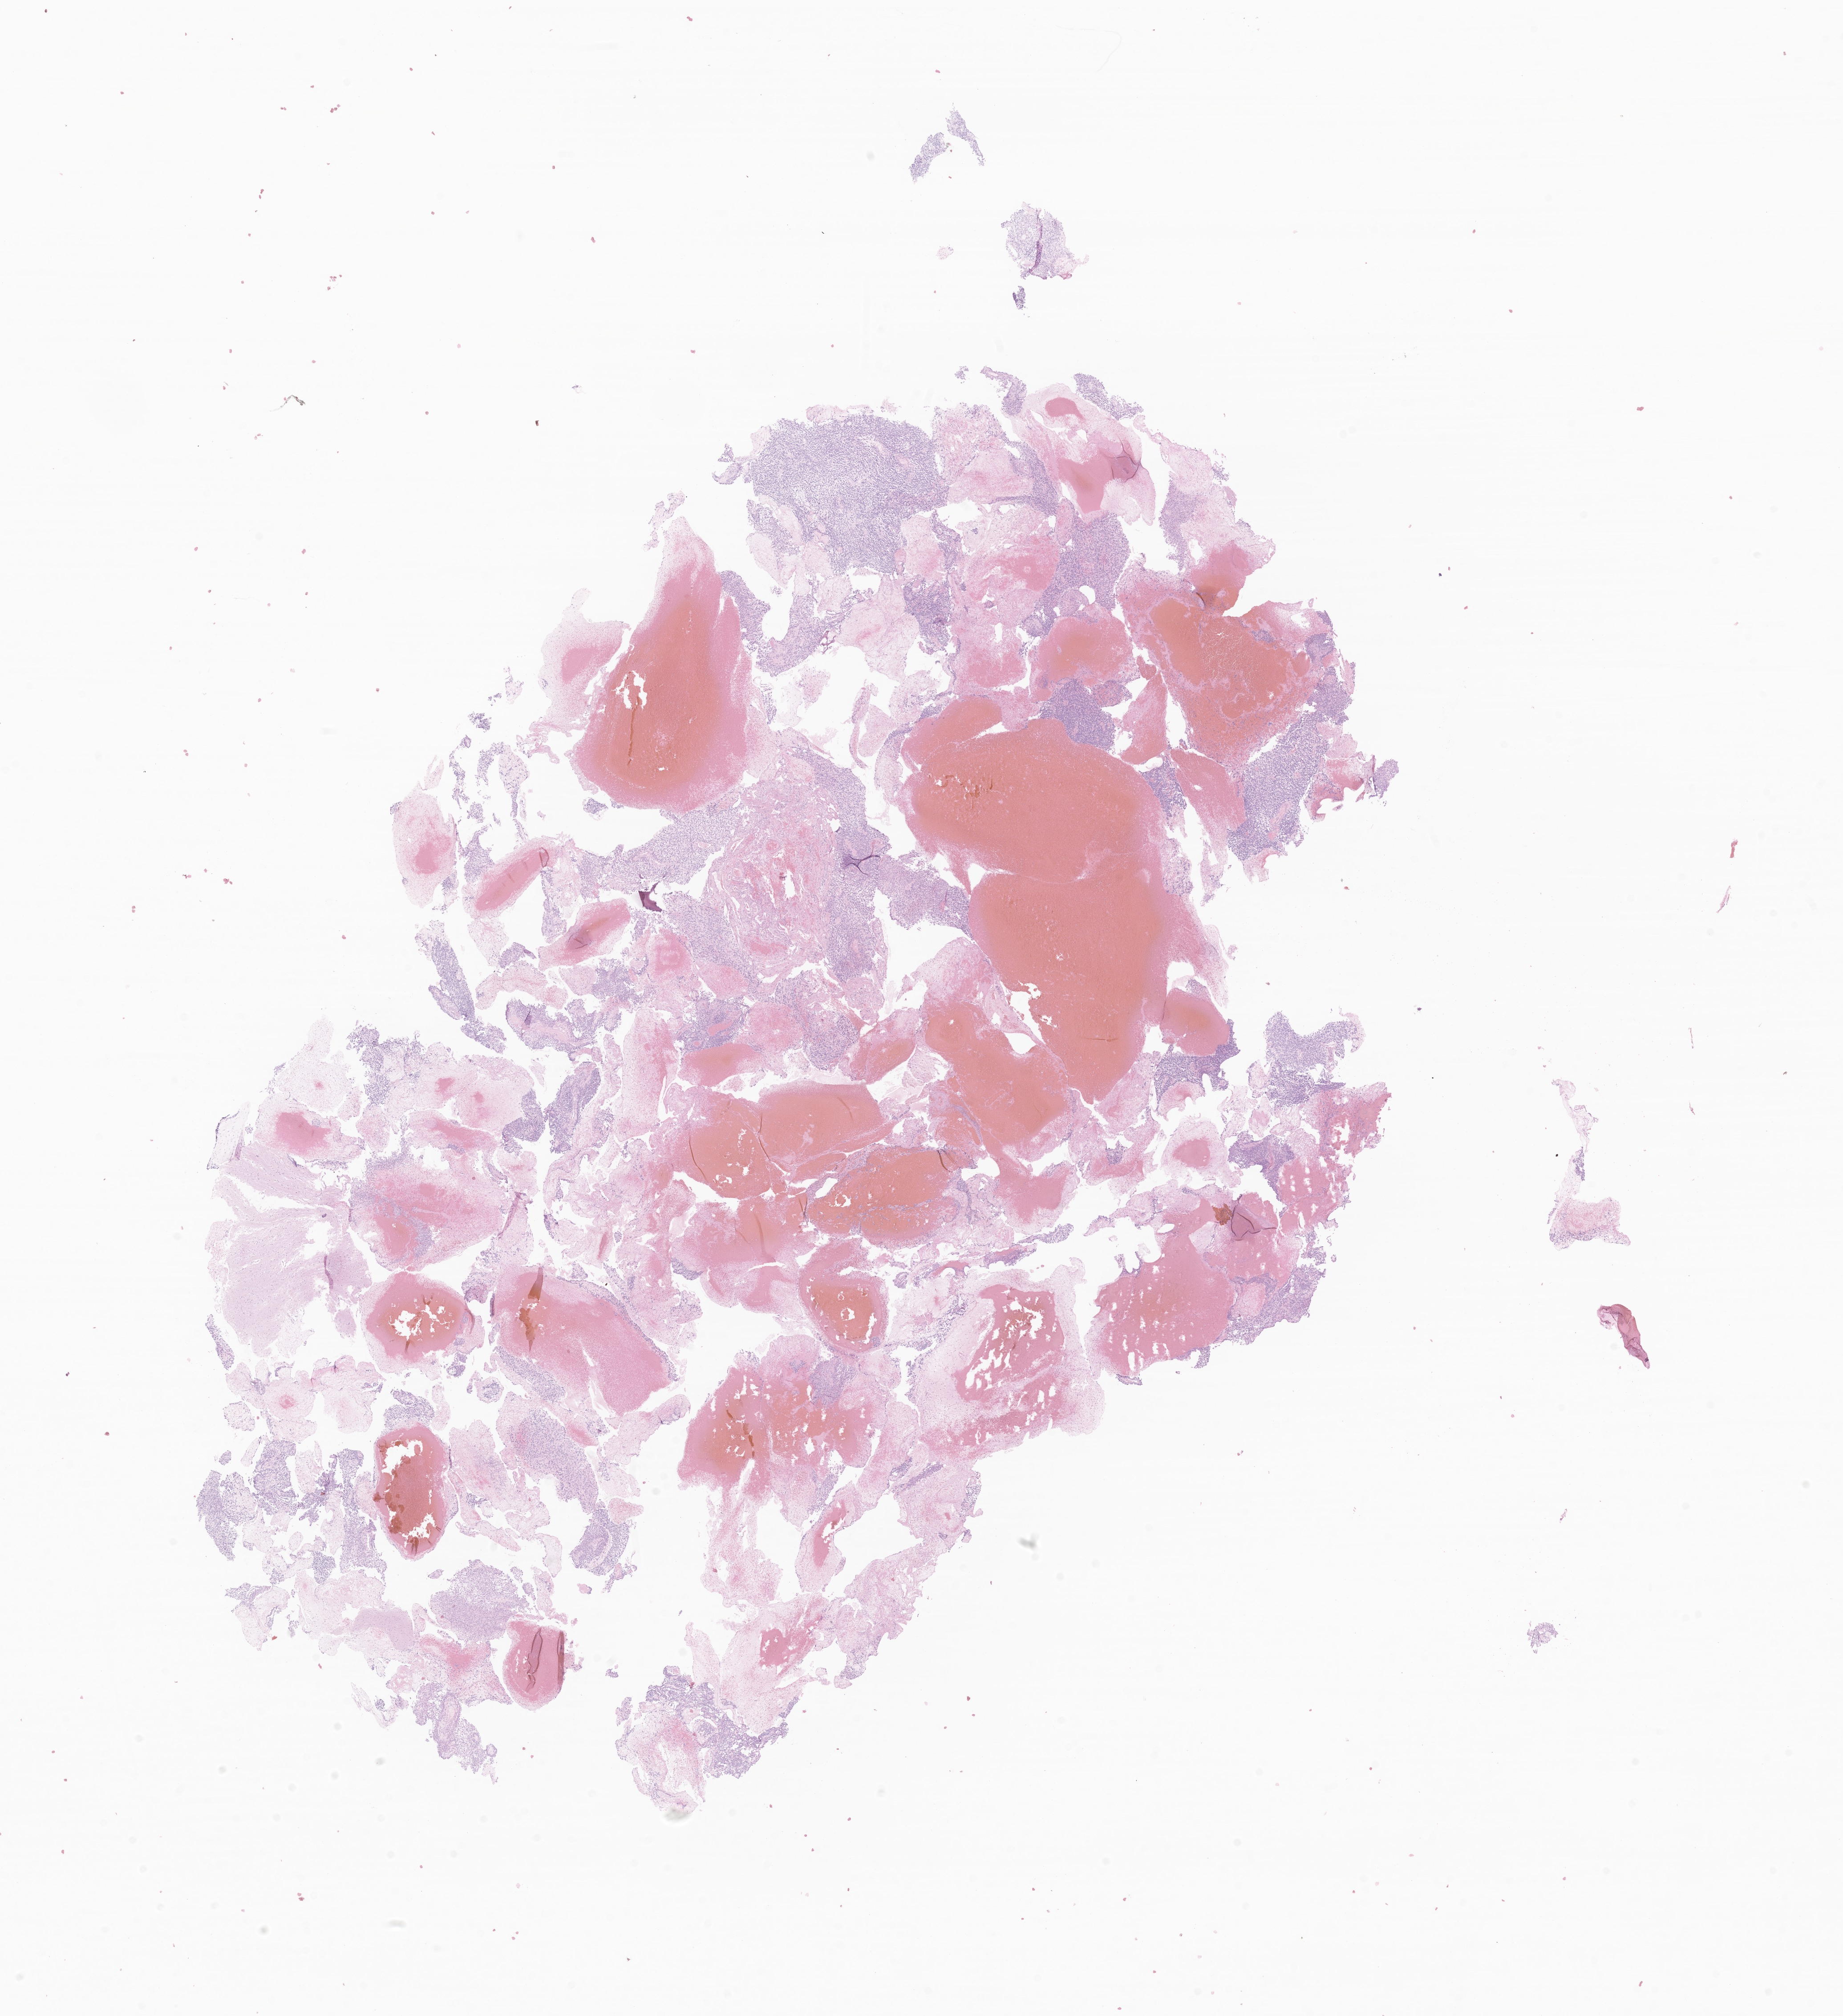
Whole-slide image, H&E stain of tumor tissue from the cerebrum, a low-resolution overview of the entire scanned area, about 17.5 x 19.1 mm; FFPE section. Patient: male, age 109 months (9 years 1 month).
Diagnosis: Glioma, malignant.